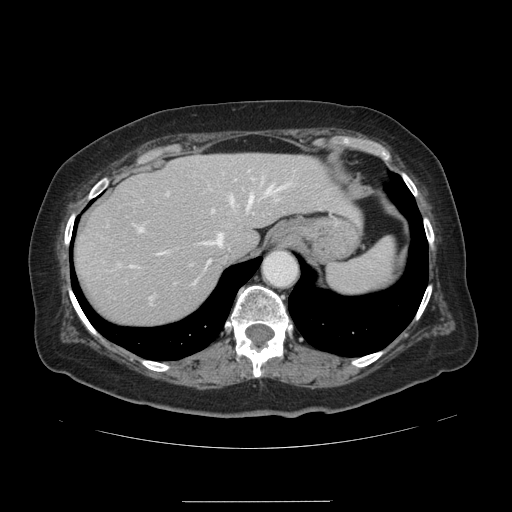
Contrast-enhanced abdominal CT, one axial slice. Slice 106 of 141 in the series (ordered by position). 120 kVp. Intravenous contrast given. Soft-tissue window (W 400 / L 40 HU). 2.5 mm slice thickness. 512 × 512 image matrix, field of view 393 × 393 mm. Female patient, age 74 years. Case-level facts recorded for this patient, not image findings: diagnosis: colorectal cancer liver metastases, imaged before liver resection.
Outlined on this slice (manually delineated by an expert):
- hepatic veins: bounding box (x1, y1, x2, y2) in pixels: (155, 186, 283, 284)
- liver: (75, 153, 355, 326)
- planned liver remnant (the part of the liver to remain after resection): (75, 153, 355, 326)
- portal vein (with intrahepatic branches): (129, 178, 253, 268)